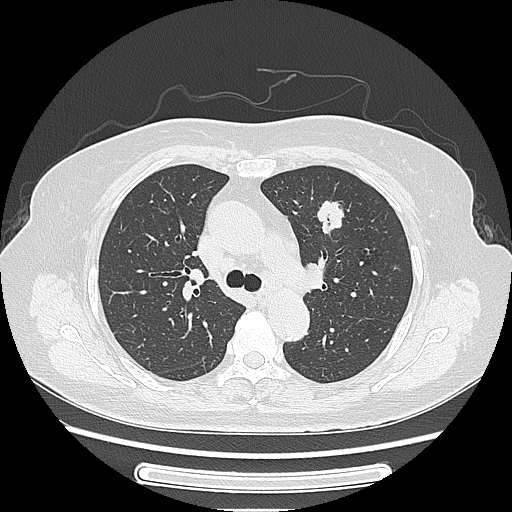
Chest CT, one axial slice. Slice 162 of 227 in the series (ordered by position). 120 kVp. Lung window (W 1500 / L -600 HU). 1.25 mm slice thickness. 512 × 512 image matrix, field of view 363 × 363 mm. Female patient, age 77 years. Case-level facts recorded for this patient, not image findings: clinical TNM (as recorded): T1c N3 M0.
Structures marked on this image (rectangle marked by the reading radiologist):
- lung tumour (recorded histology: adenocarcinoma): bounding box <311,188,351,241> (left, top, right, bottom; pixels)